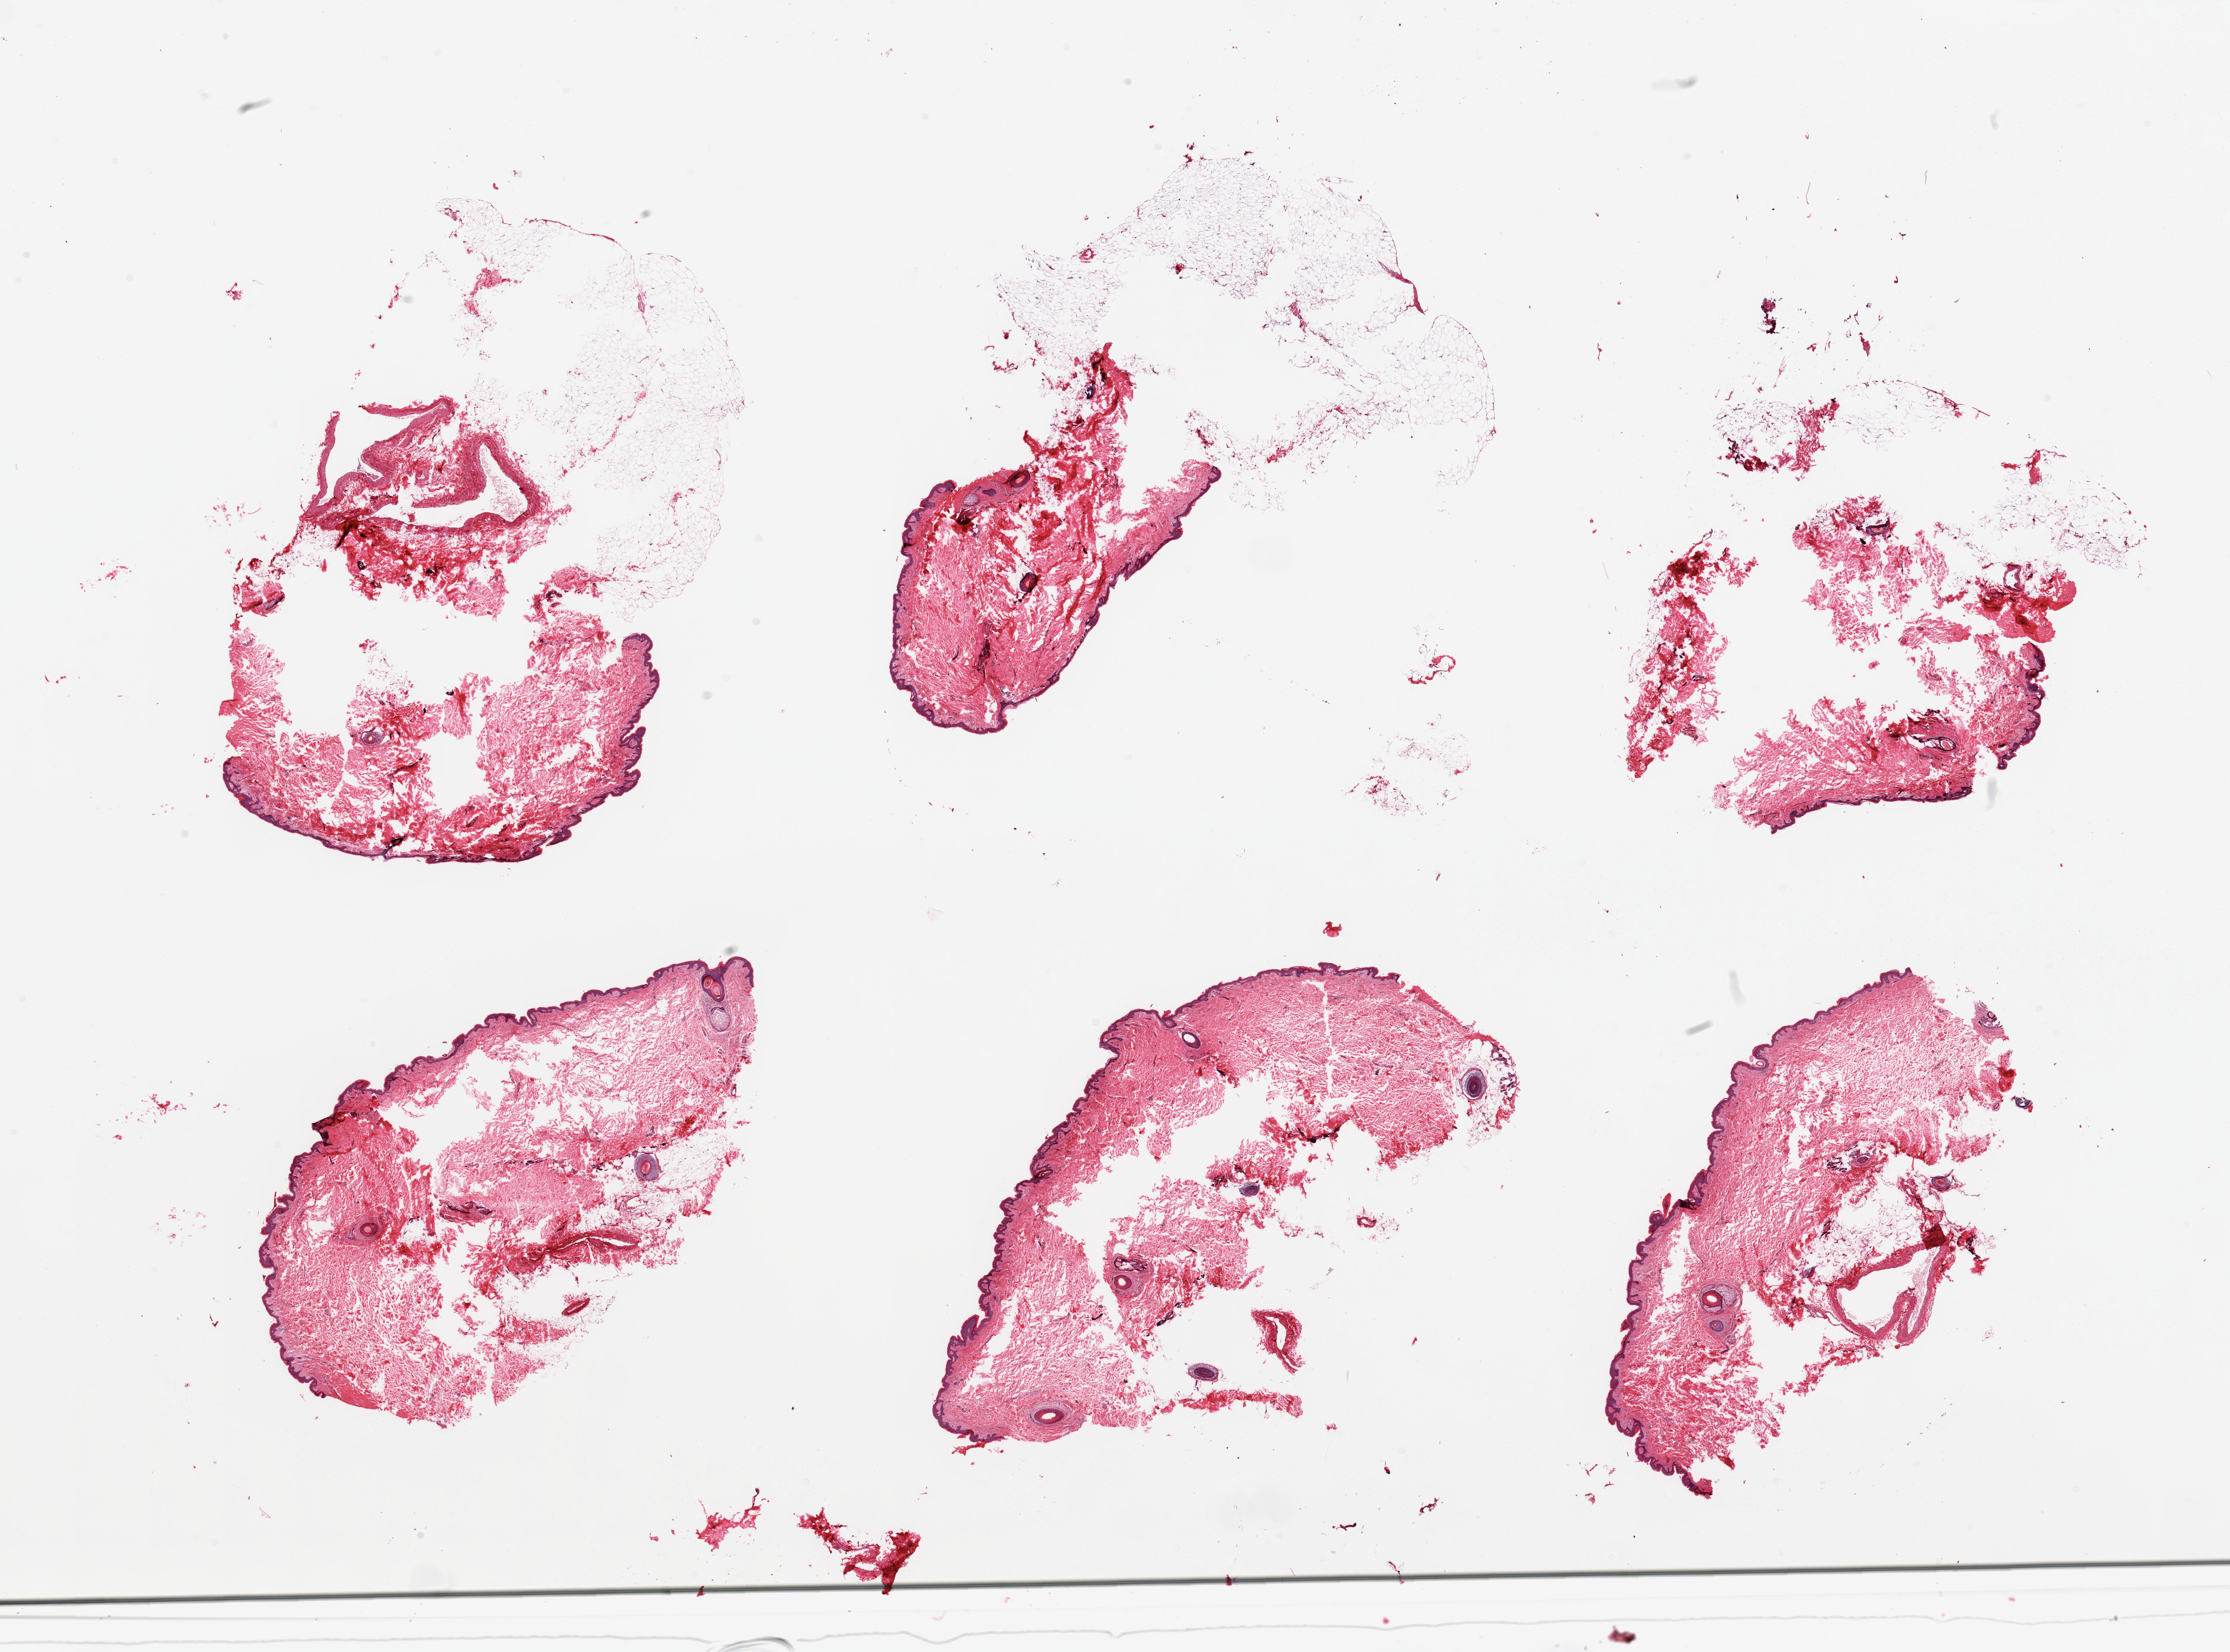
Digitized hematoxylin and eosin (H&E)-stained section, whole scanned area (about 29.5 x 21.9 mm) shown as a low-resolution overview; PAXgene-fixed paraffin-embedded (PFPE) section; section of skin of suprapubic region (target tissue); donor tissue sample. Donor: male.
Review note (as recorded): 6 pieces; include up to 50% attached fat, incomplete sections (?poor fixation).